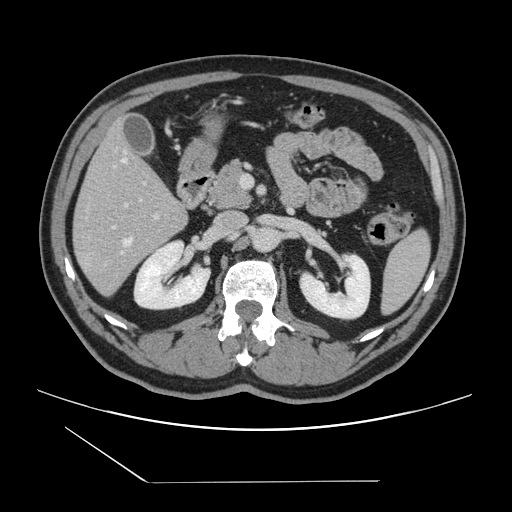
Contrast-enhanced abdominal CT, one axial slice. 120 kVp. Soft-tissue window (W 400 / L 40 HU). 2.5 mm slice thickness. 512 × 512 image matrix, field of view 407 × 407 mm. Male patient, age 61 years. From the clinical record (not read from this slice): diagnosis: colorectal cancer liver metastases, imaged before liver resection; multiple liver metastases: yes; largest metastasis: 5.5 cm; chemotherapy before resection: no.
Outlined on this slice (expert manual segmentation):
- hepatic veins: bounding box [x1, y1, x2, y2] px = [122, 158, 141, 253]
- liver: [74, 126, 187, 296]
- planned liver remnant (the part of the liver to remain after resection): [76, 125, 177, 218]
- portal vein (with intrahepatic branches): [113, 203, 159, 228]